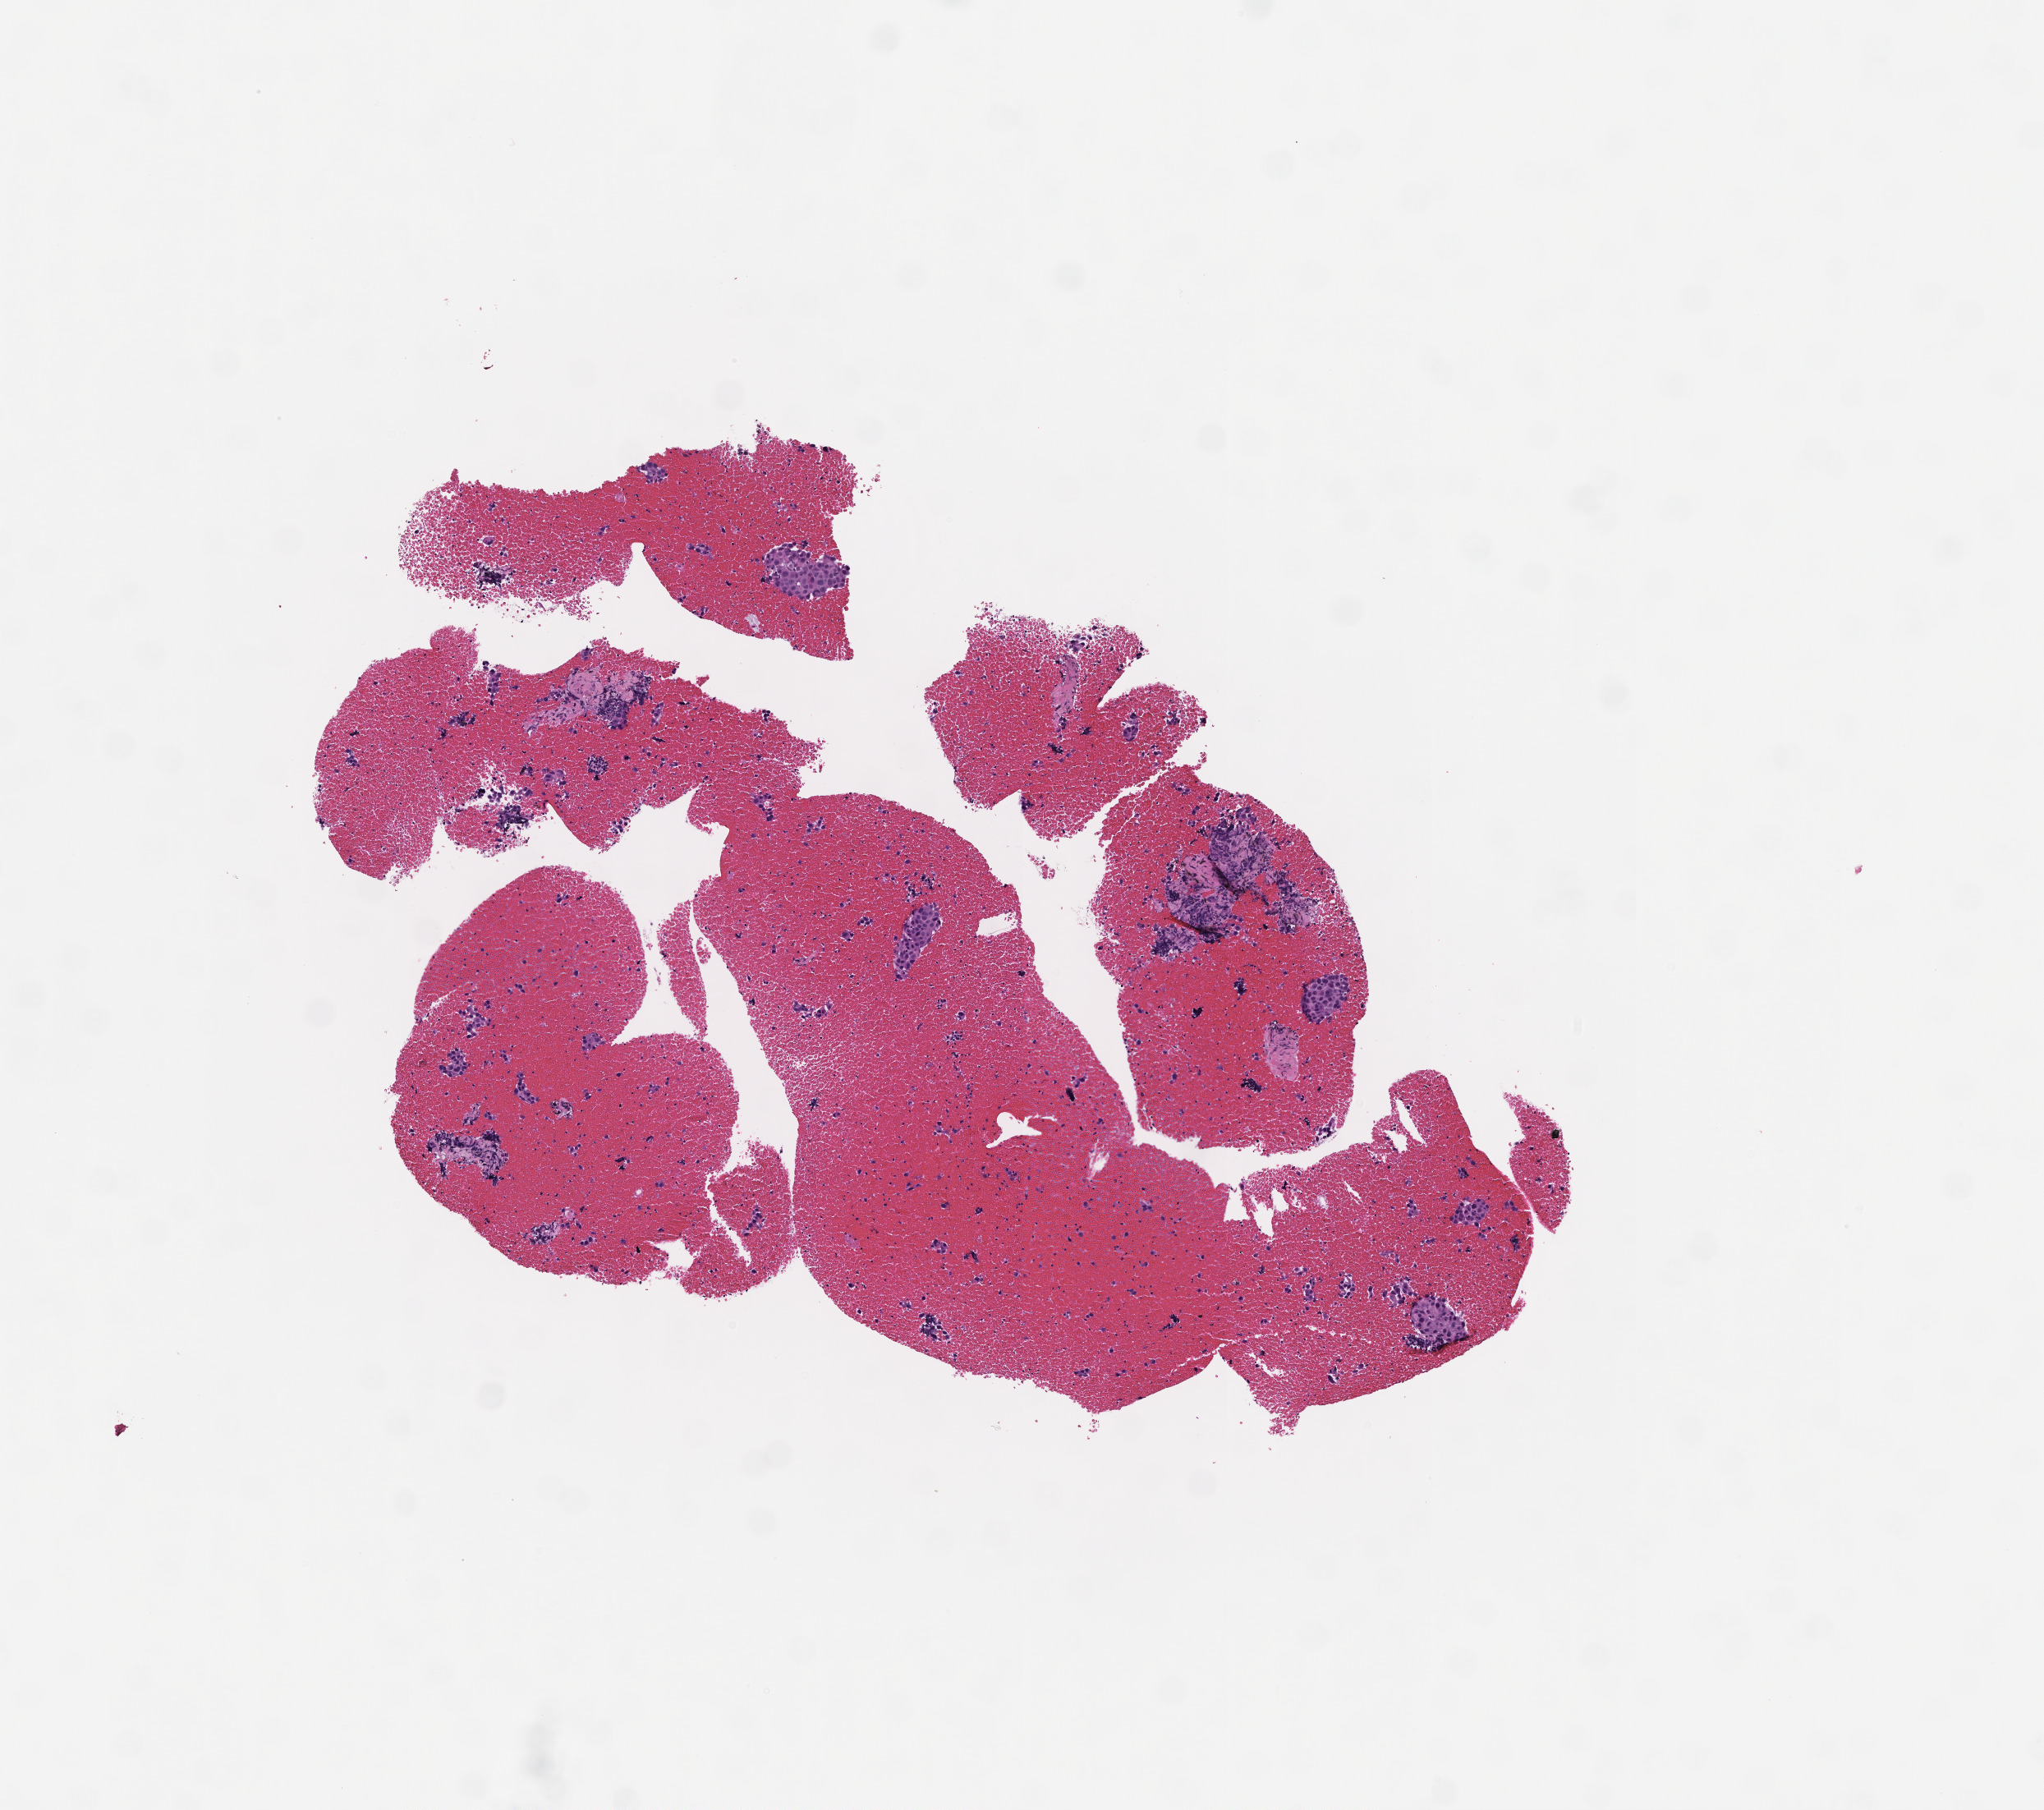
Digitized hematoxylin and eosin (H&E)-stained section, low-resolution overview of the scanned area, about 5.0 x 4.5 mm; formalin-fixed, paraffin-embedded (FFPE) tissue; site: lung. Patient: female.
This section: primary tumor. Diagnosis: Non-Small Cell Lung Carcinoma.